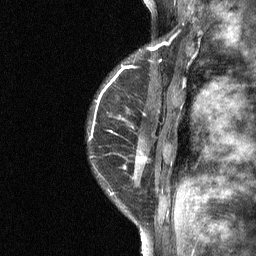
Breast MRI (dynamic contrast-enhanced), one sagittal slice. Slice 15 of 64 in the series (ordered by position). Dynamic contrast-enhanced study with each time point stored as its own series, time point 2 of 3 at this slice position (early post-contrast, ordered by acquisition time). 1.5 T. TE 4.8 ms, TR 27 ms. 2 mm slice thickness. 256 × 256 image matrix, field of view 180 × 180 mm. Female patient, age 34 years. Case-level facts recorded for this patient, not image findings: setting: breast cancer imaged before/during neoadjuvant chemotherapy; receptor status: HR-positive, HER2-negative.
Annotated regions visible in this slice (semi-automatically segmented with operator editing):
- analysis volume of interest (the breast-tissue region the enhancement analysis was run in; not a lesion): box from (x=87, y=44) to (x=181, y=191) px
- tumour enhancement mask (voxels above the 90 % enhancement threshold inside the analysis volume of interest): (x=110, y=46)–(x=158, y=133)